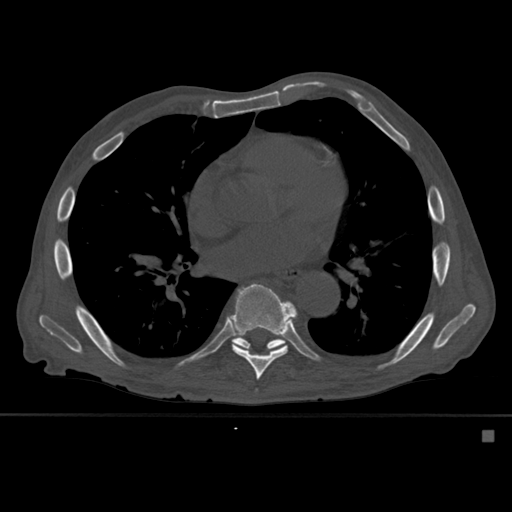
CT including the spine, one axial slice. Bone window (W 1800 / L 400 HU). 1.5 mm slice thickness. 512 × 512 image matrix, field of view 373 × 373 mm. Male patient, age 78 years. From the clinical record (not read from this slice): primary cancer: prostate.
Outlined on this slice (semi-automatically segmented with operator editing):
- T8 vertebra: bounding box <226,283,298,380> (left, top, right, bottom; pixels)
- T9 vertebra: <232,335,286,351>